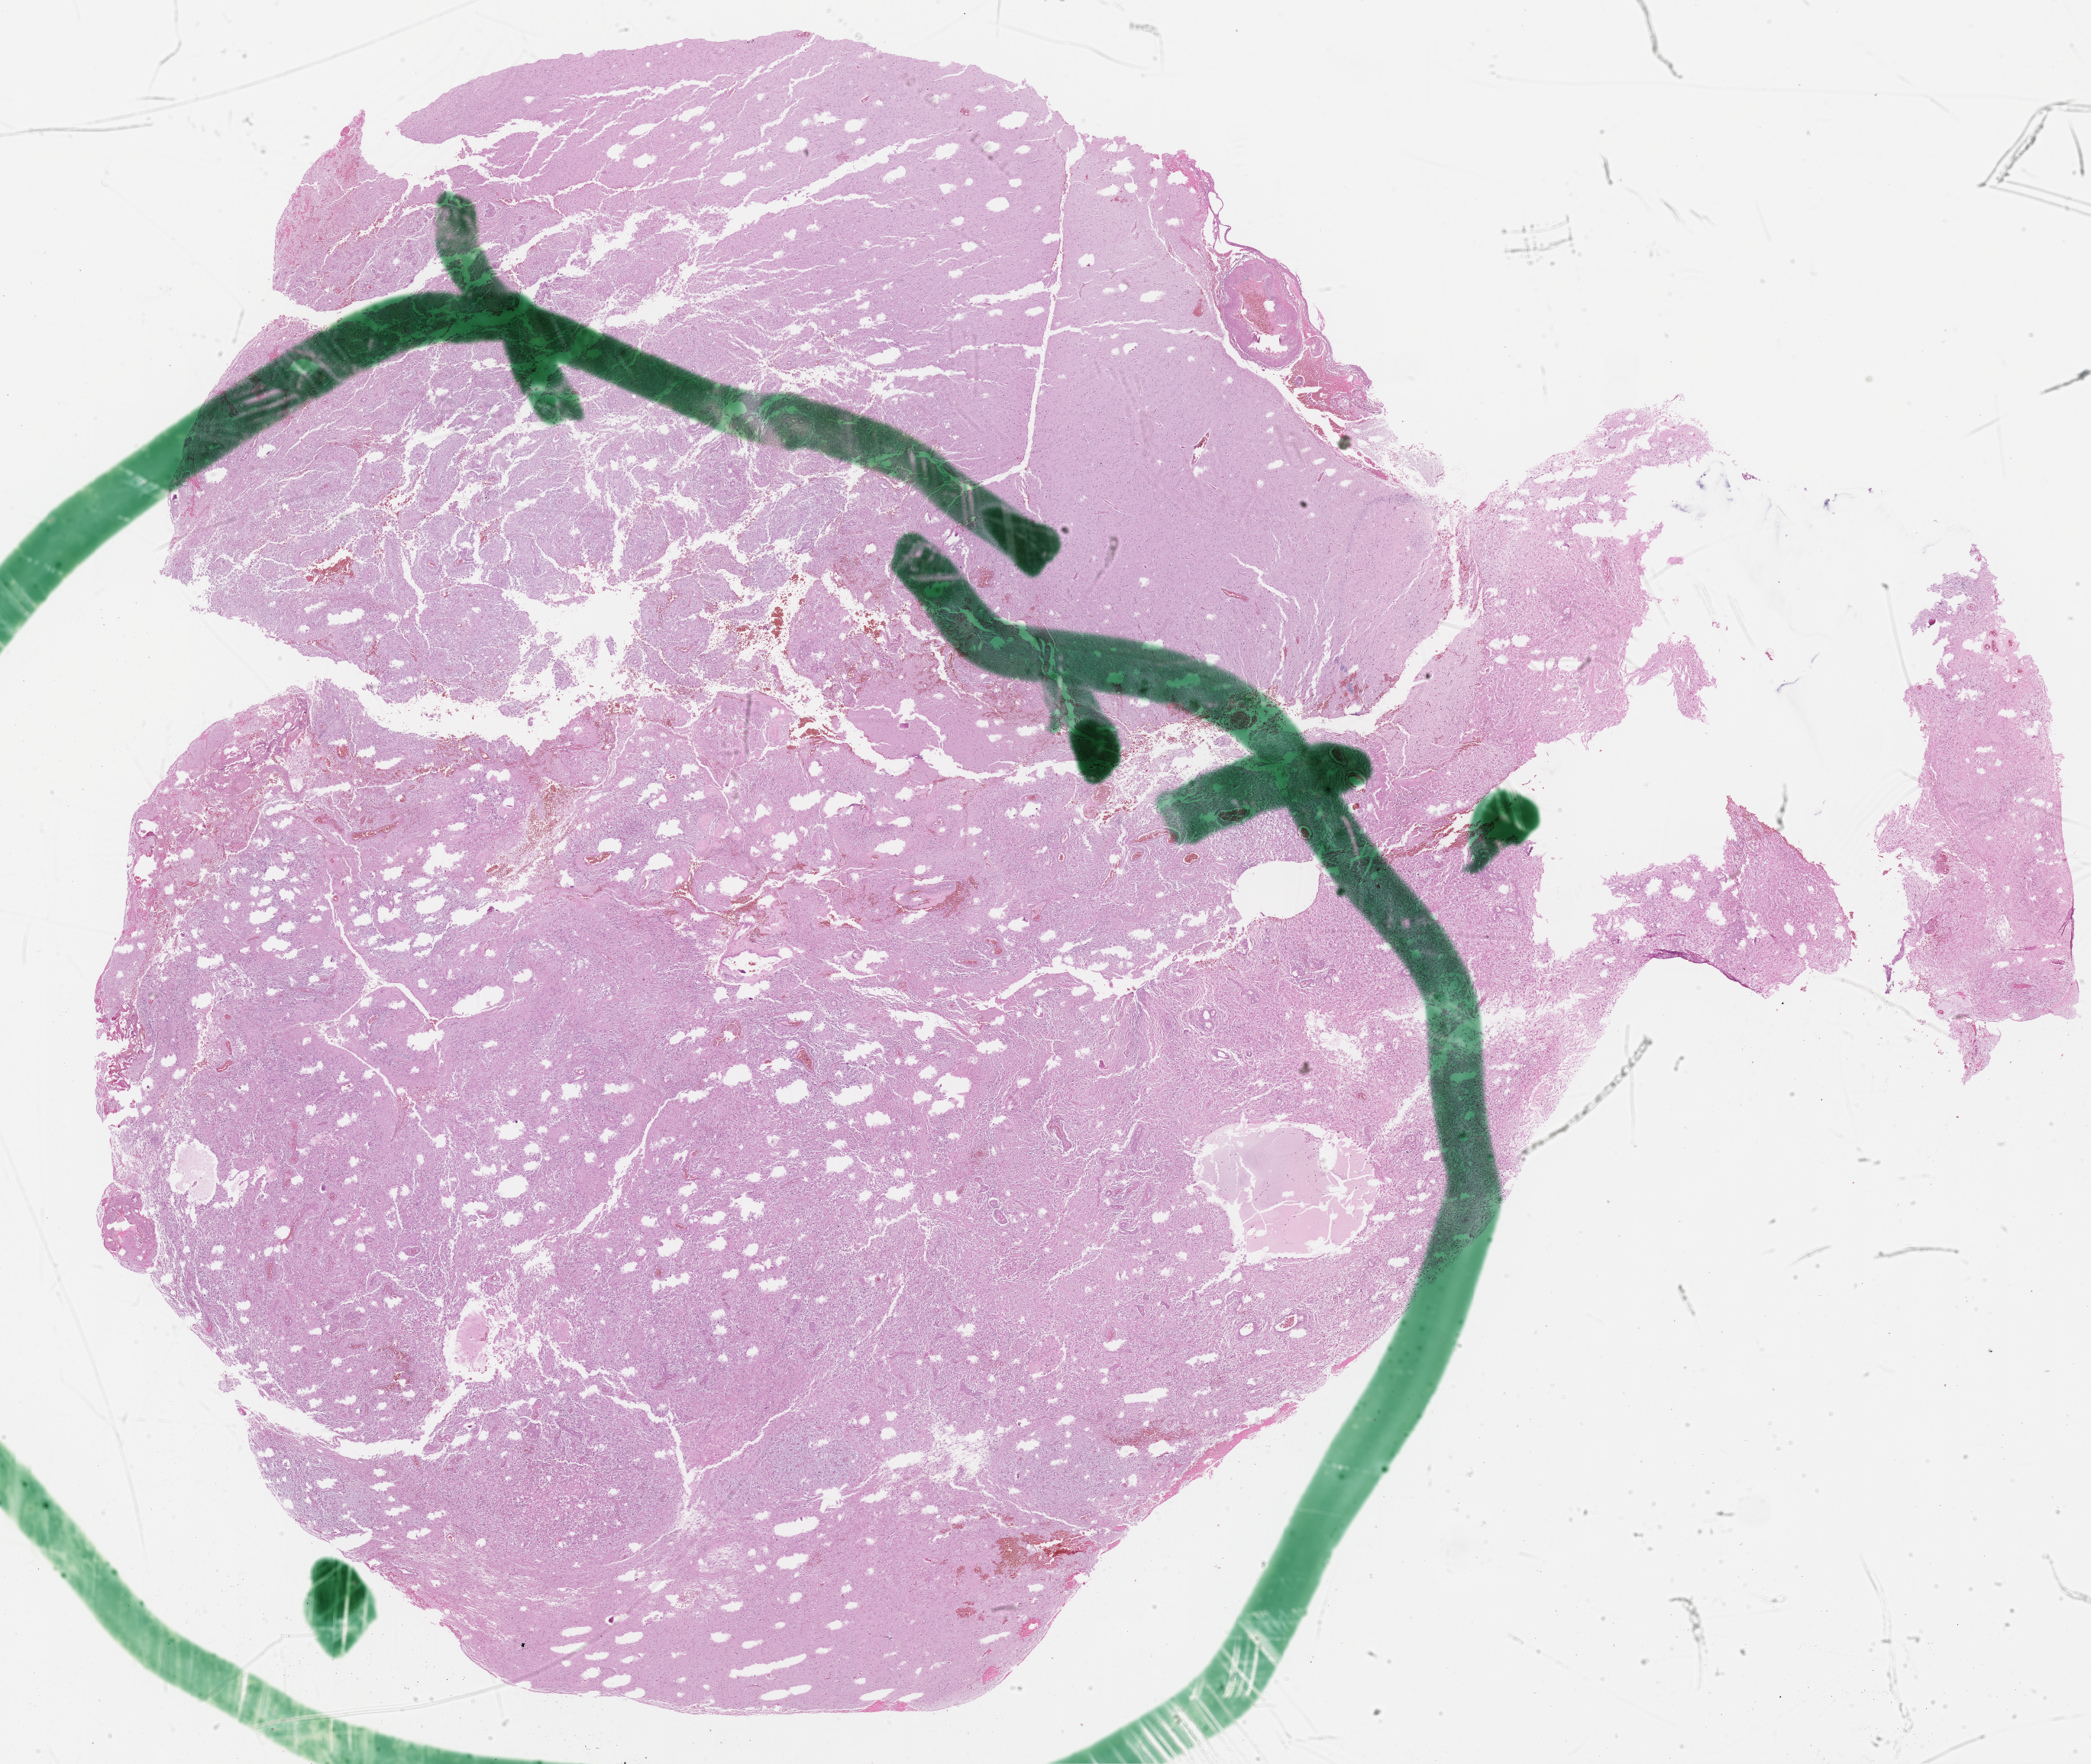
Digitized H&E tissue section (whole slide), a low-resolution overview of the entire scanned area, about 22.2 x 18.7 mm; formalin-fixed paraffin-embedded (FFPE) diagnostic section; primary tumour sample from the brain. Male patient; age at initial diagnosis 78 years.
Pathologic diagnosis: Glioblastoma.